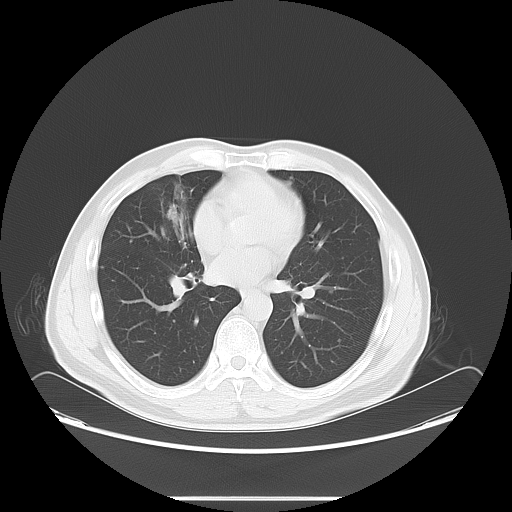
Chest CT, one axial slice; slice 37 of 73 in the series (ordered by position); reconstruction kernel LUNG; 120 kVp; lung window (W 1500 / L -600 HU); 5 mm slice thickness; 512 × 512 image matrix. Patient: male, 47 years. From the clinical record (not read from this slice): clinical TNM (as recorded): T1c N3 M0.
Annotated regions visible in this slice (bounding box drawn by a radiologist):
- lung tumour (recorded histology: adenocarcinoma): box from (x=161, y=174) to (x=201, y=230) px